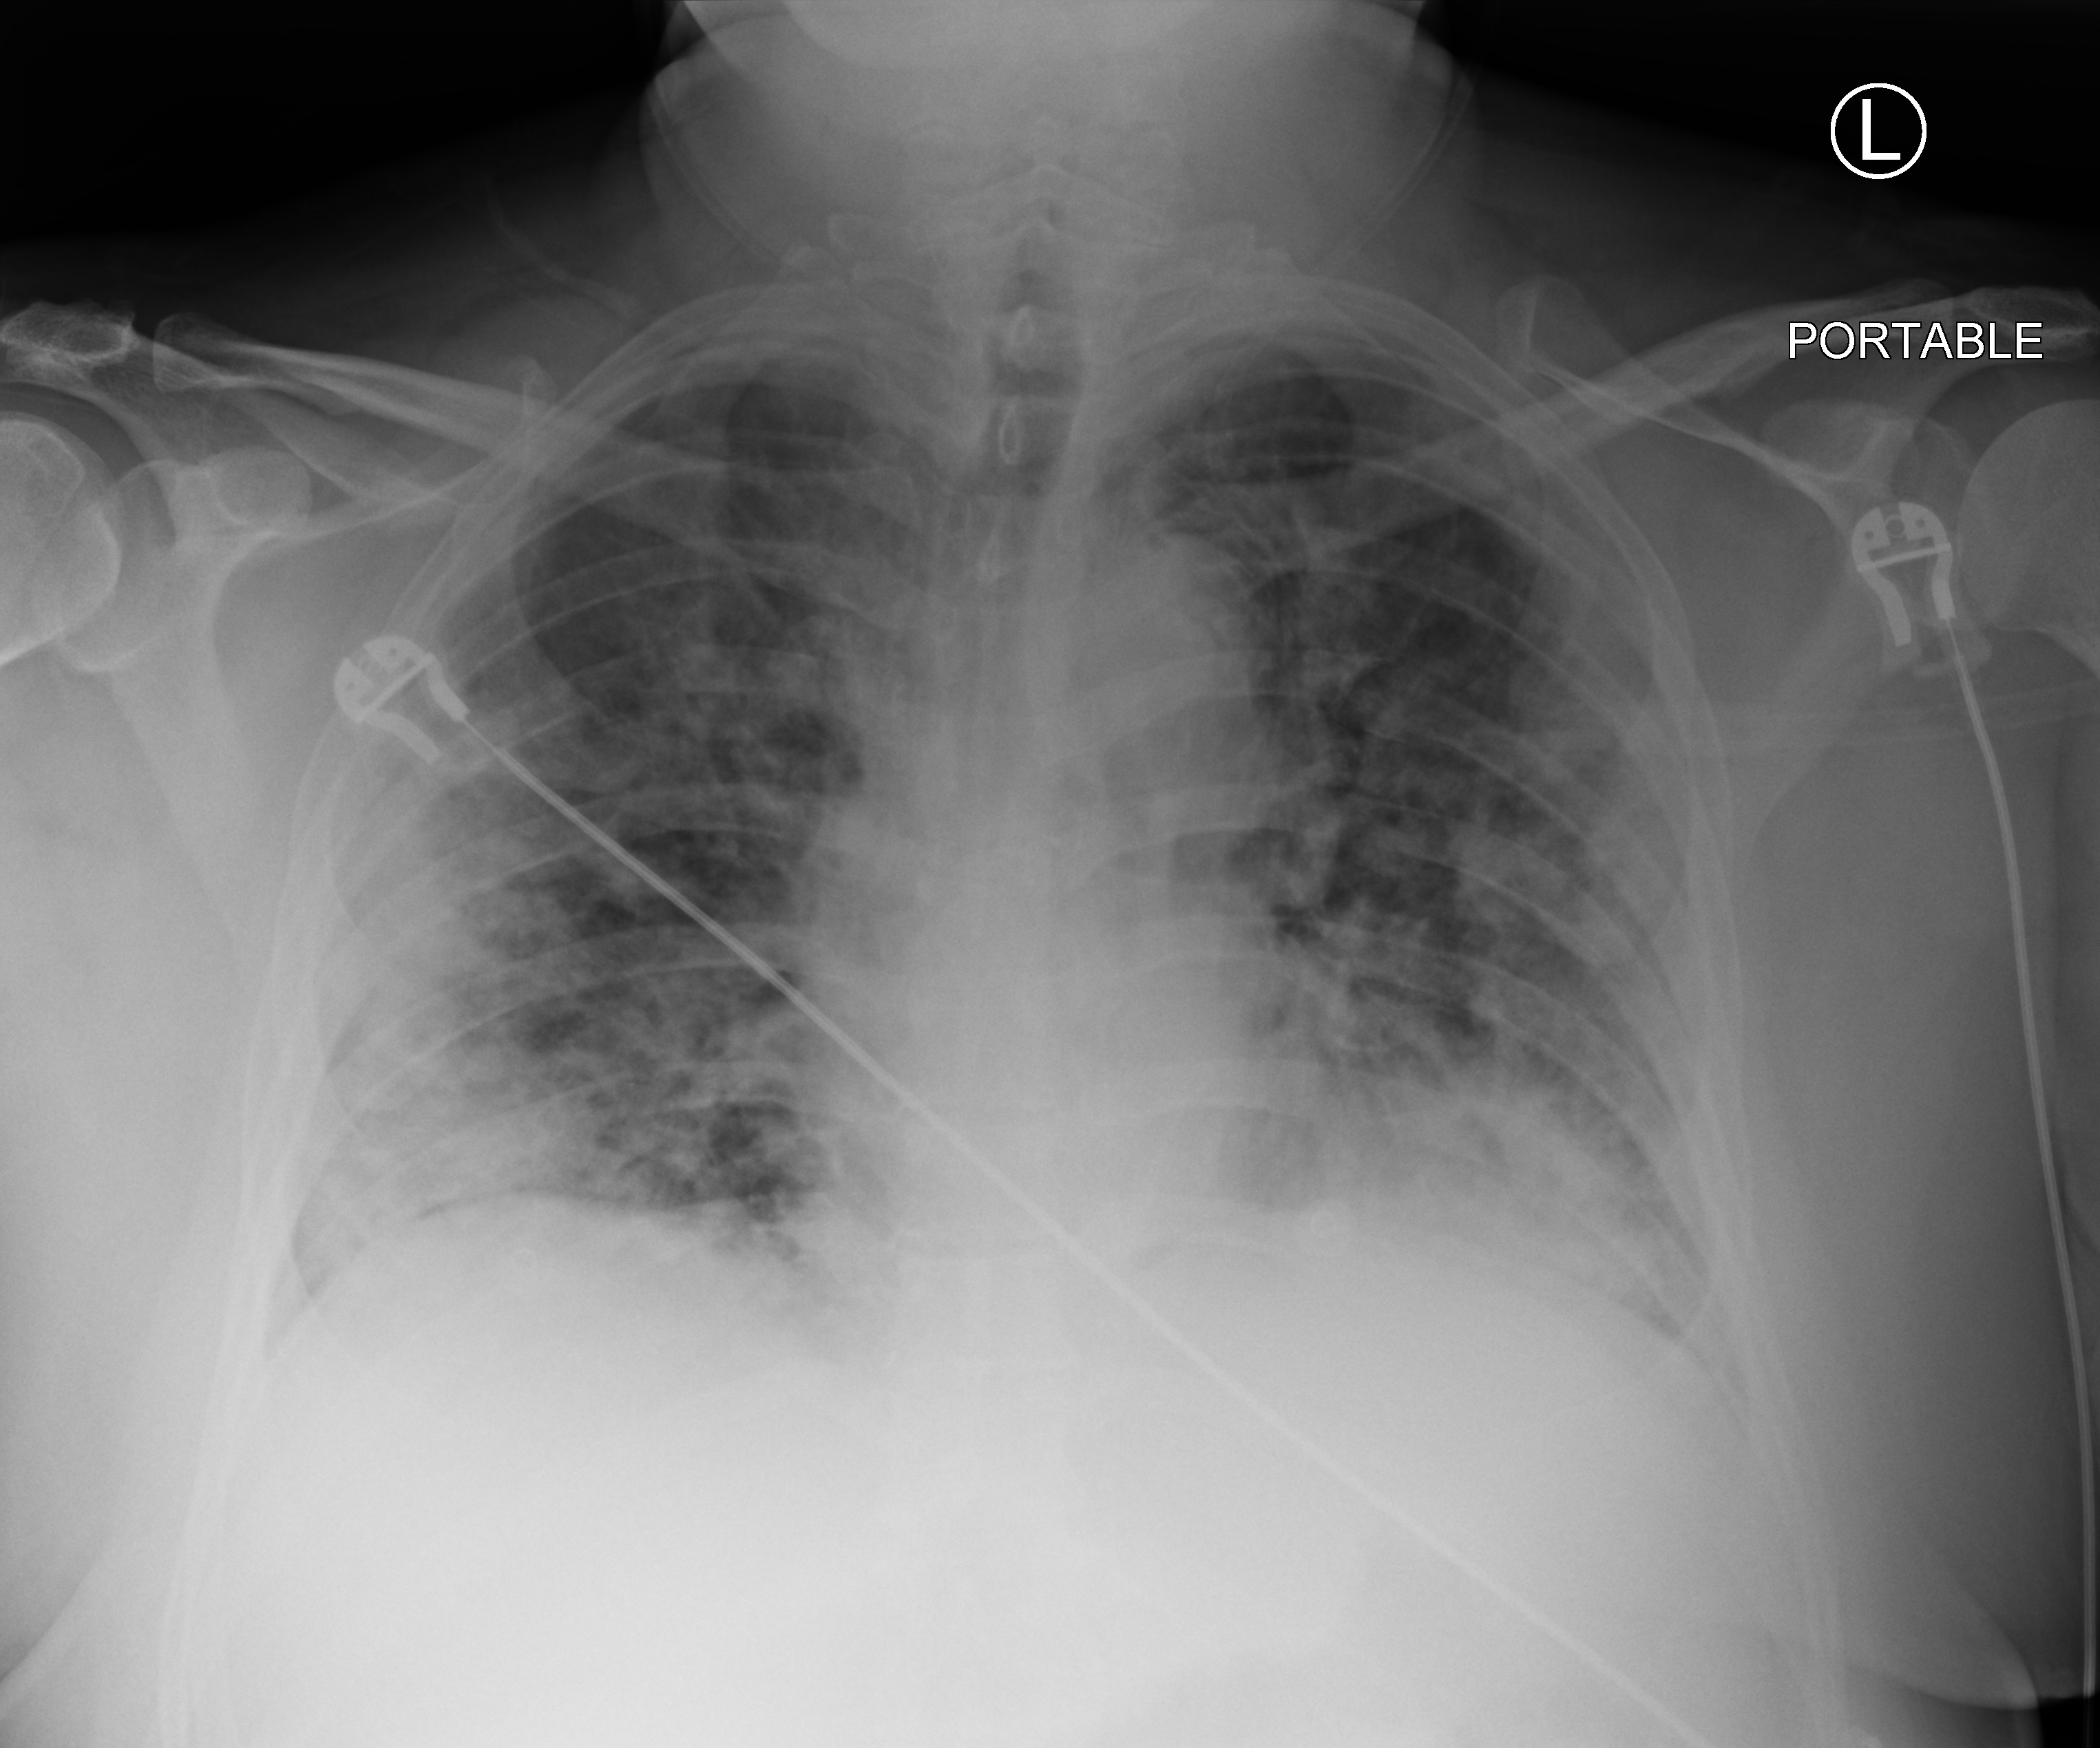
Bedside chest radiograph (computed radiography); anteroposterior (AP) projection. Male patient hospitalised with COVID-19, age 18–59 years.
Admission-level facts for this patient (not findings on this image; timing relative to this image not recorded):
- length of hospital stay: 8 days
- diabetes (admission record): yes
- smoking status (admission record): never